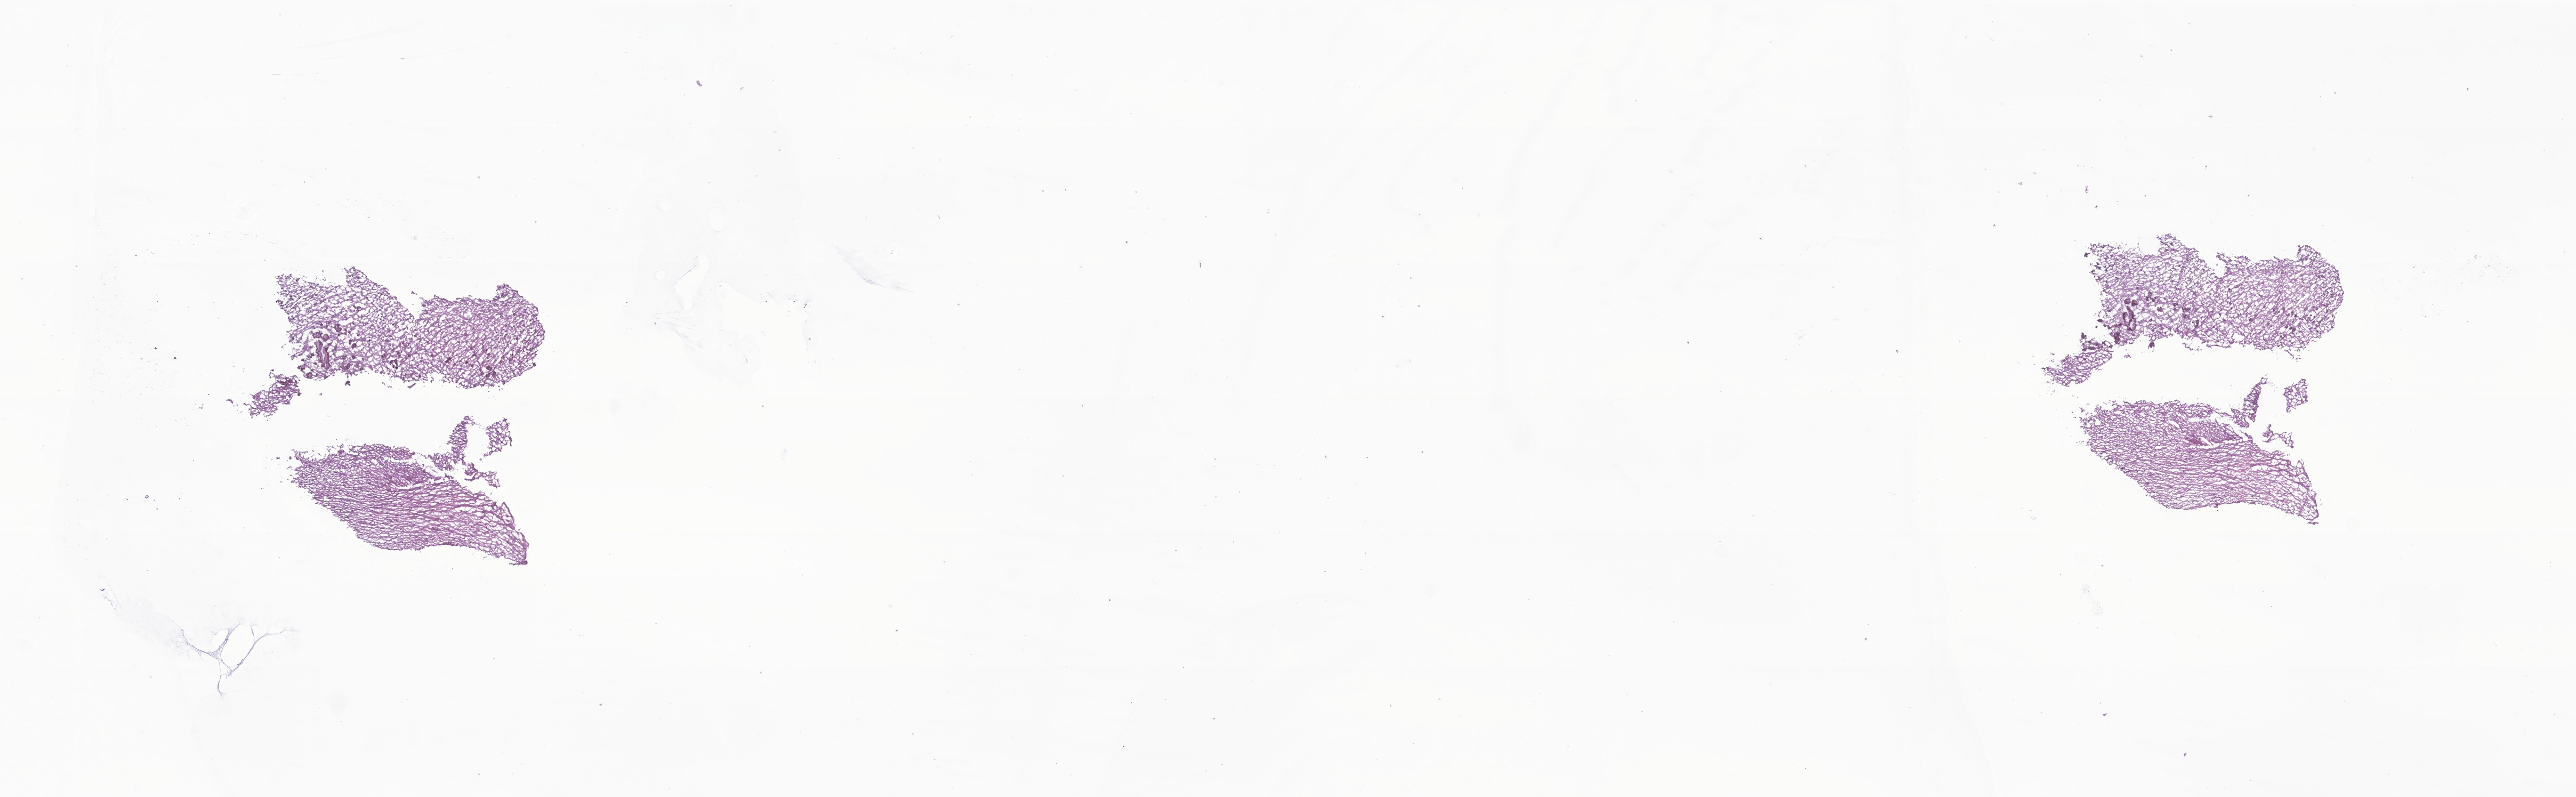
Whole-slide image, H&E stain of tumor tissue from the cerebellum — low-resolution overview of the scanned area, about 20.4 x 6.3 mm; frozen section. Male patient, age 191 months (15 years 11 months).
- diagnosis: Glioma, malignant